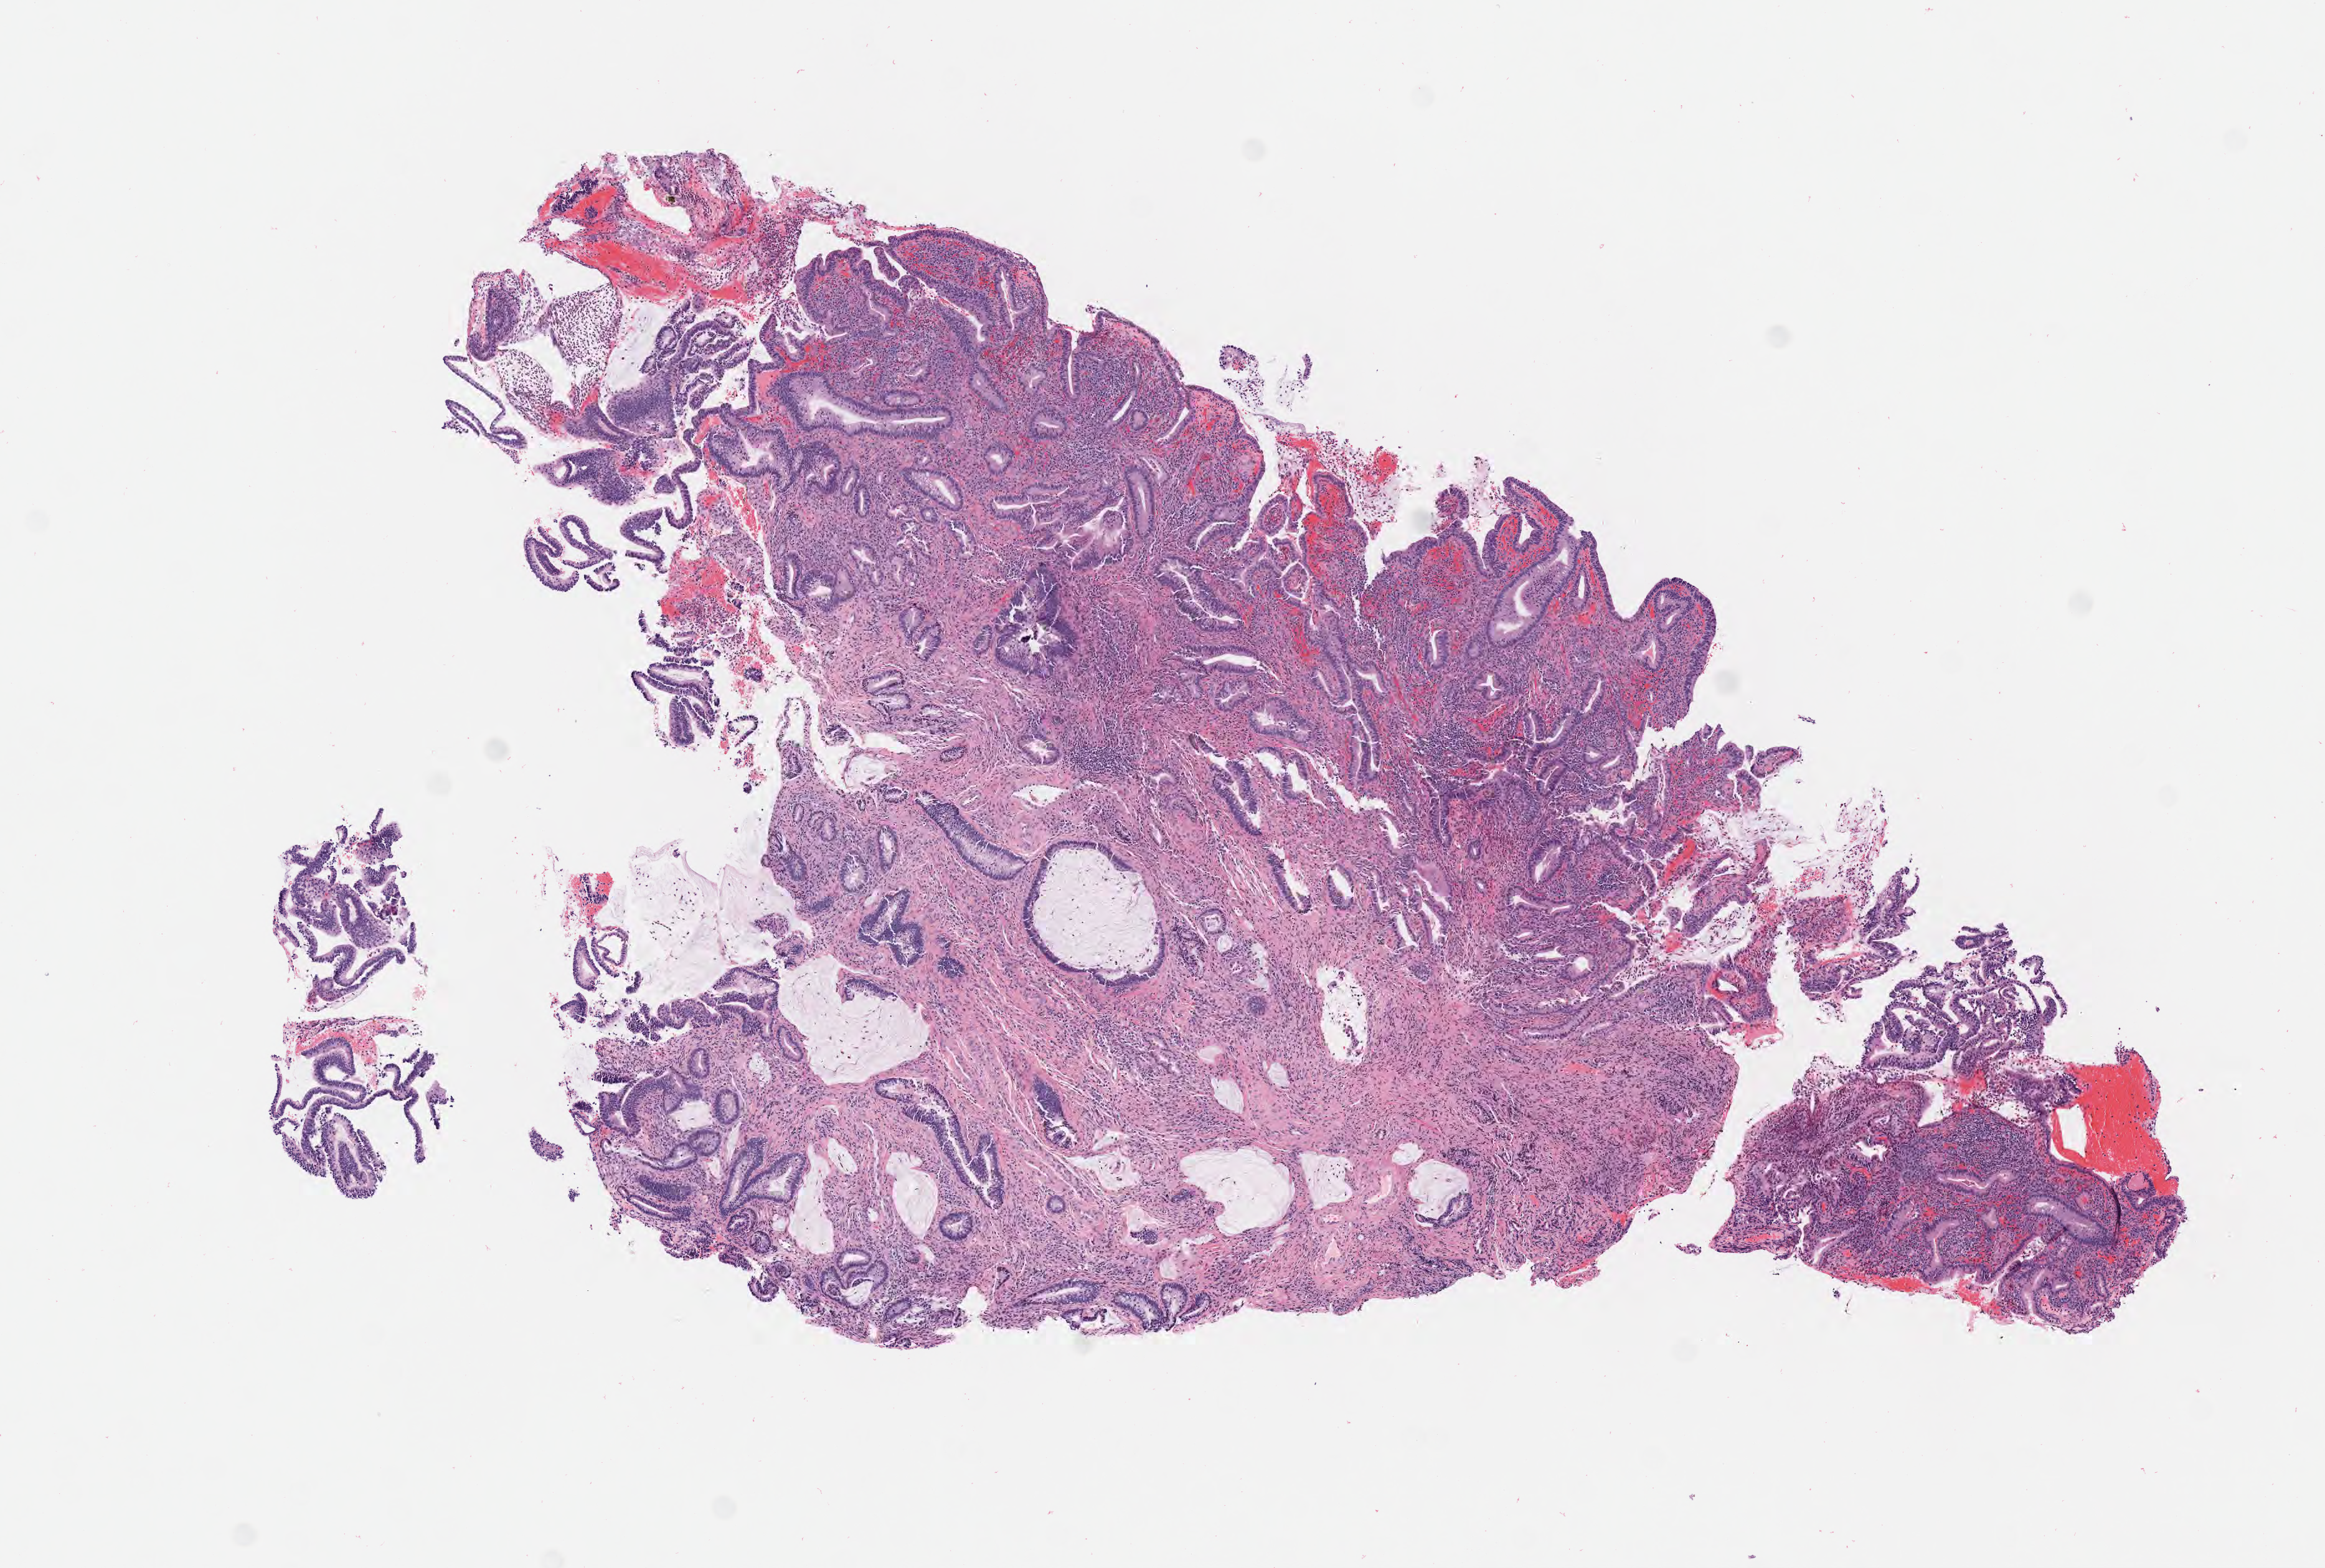
H&E whole-slide image — low-resolution overview of the scanned area, about 7.6 x 5.1 mm; tumor tissue; anatomic site: cervix. Patient: female, age 36 years.
* histologic diagnosis: Adenocarcinoma, NOS